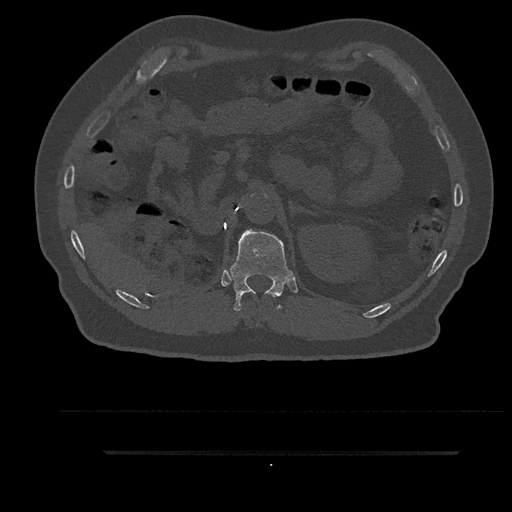
CT including the spine, one axial slice; position 253 of 797 along the scan axis; reconstruction kernel Br40s/3; bone window (W 1800 / L 400 HU); 0.5 mm slice thickness; 512 × 512 image matrix, field of view 432 × 432 mm. Patient: male, 63 years. Case-level facts recorded for this patient, not image findings: primary cancer: renal; vertebrae with lytic lesions (as recorded): T8.
Structures marked on this image (semi-automatic segmentation, software-assisted and operator-edited):
- T12 vertebra: bounding box [x1, y1, x2, y2] px = [227, 229, 293, 311]